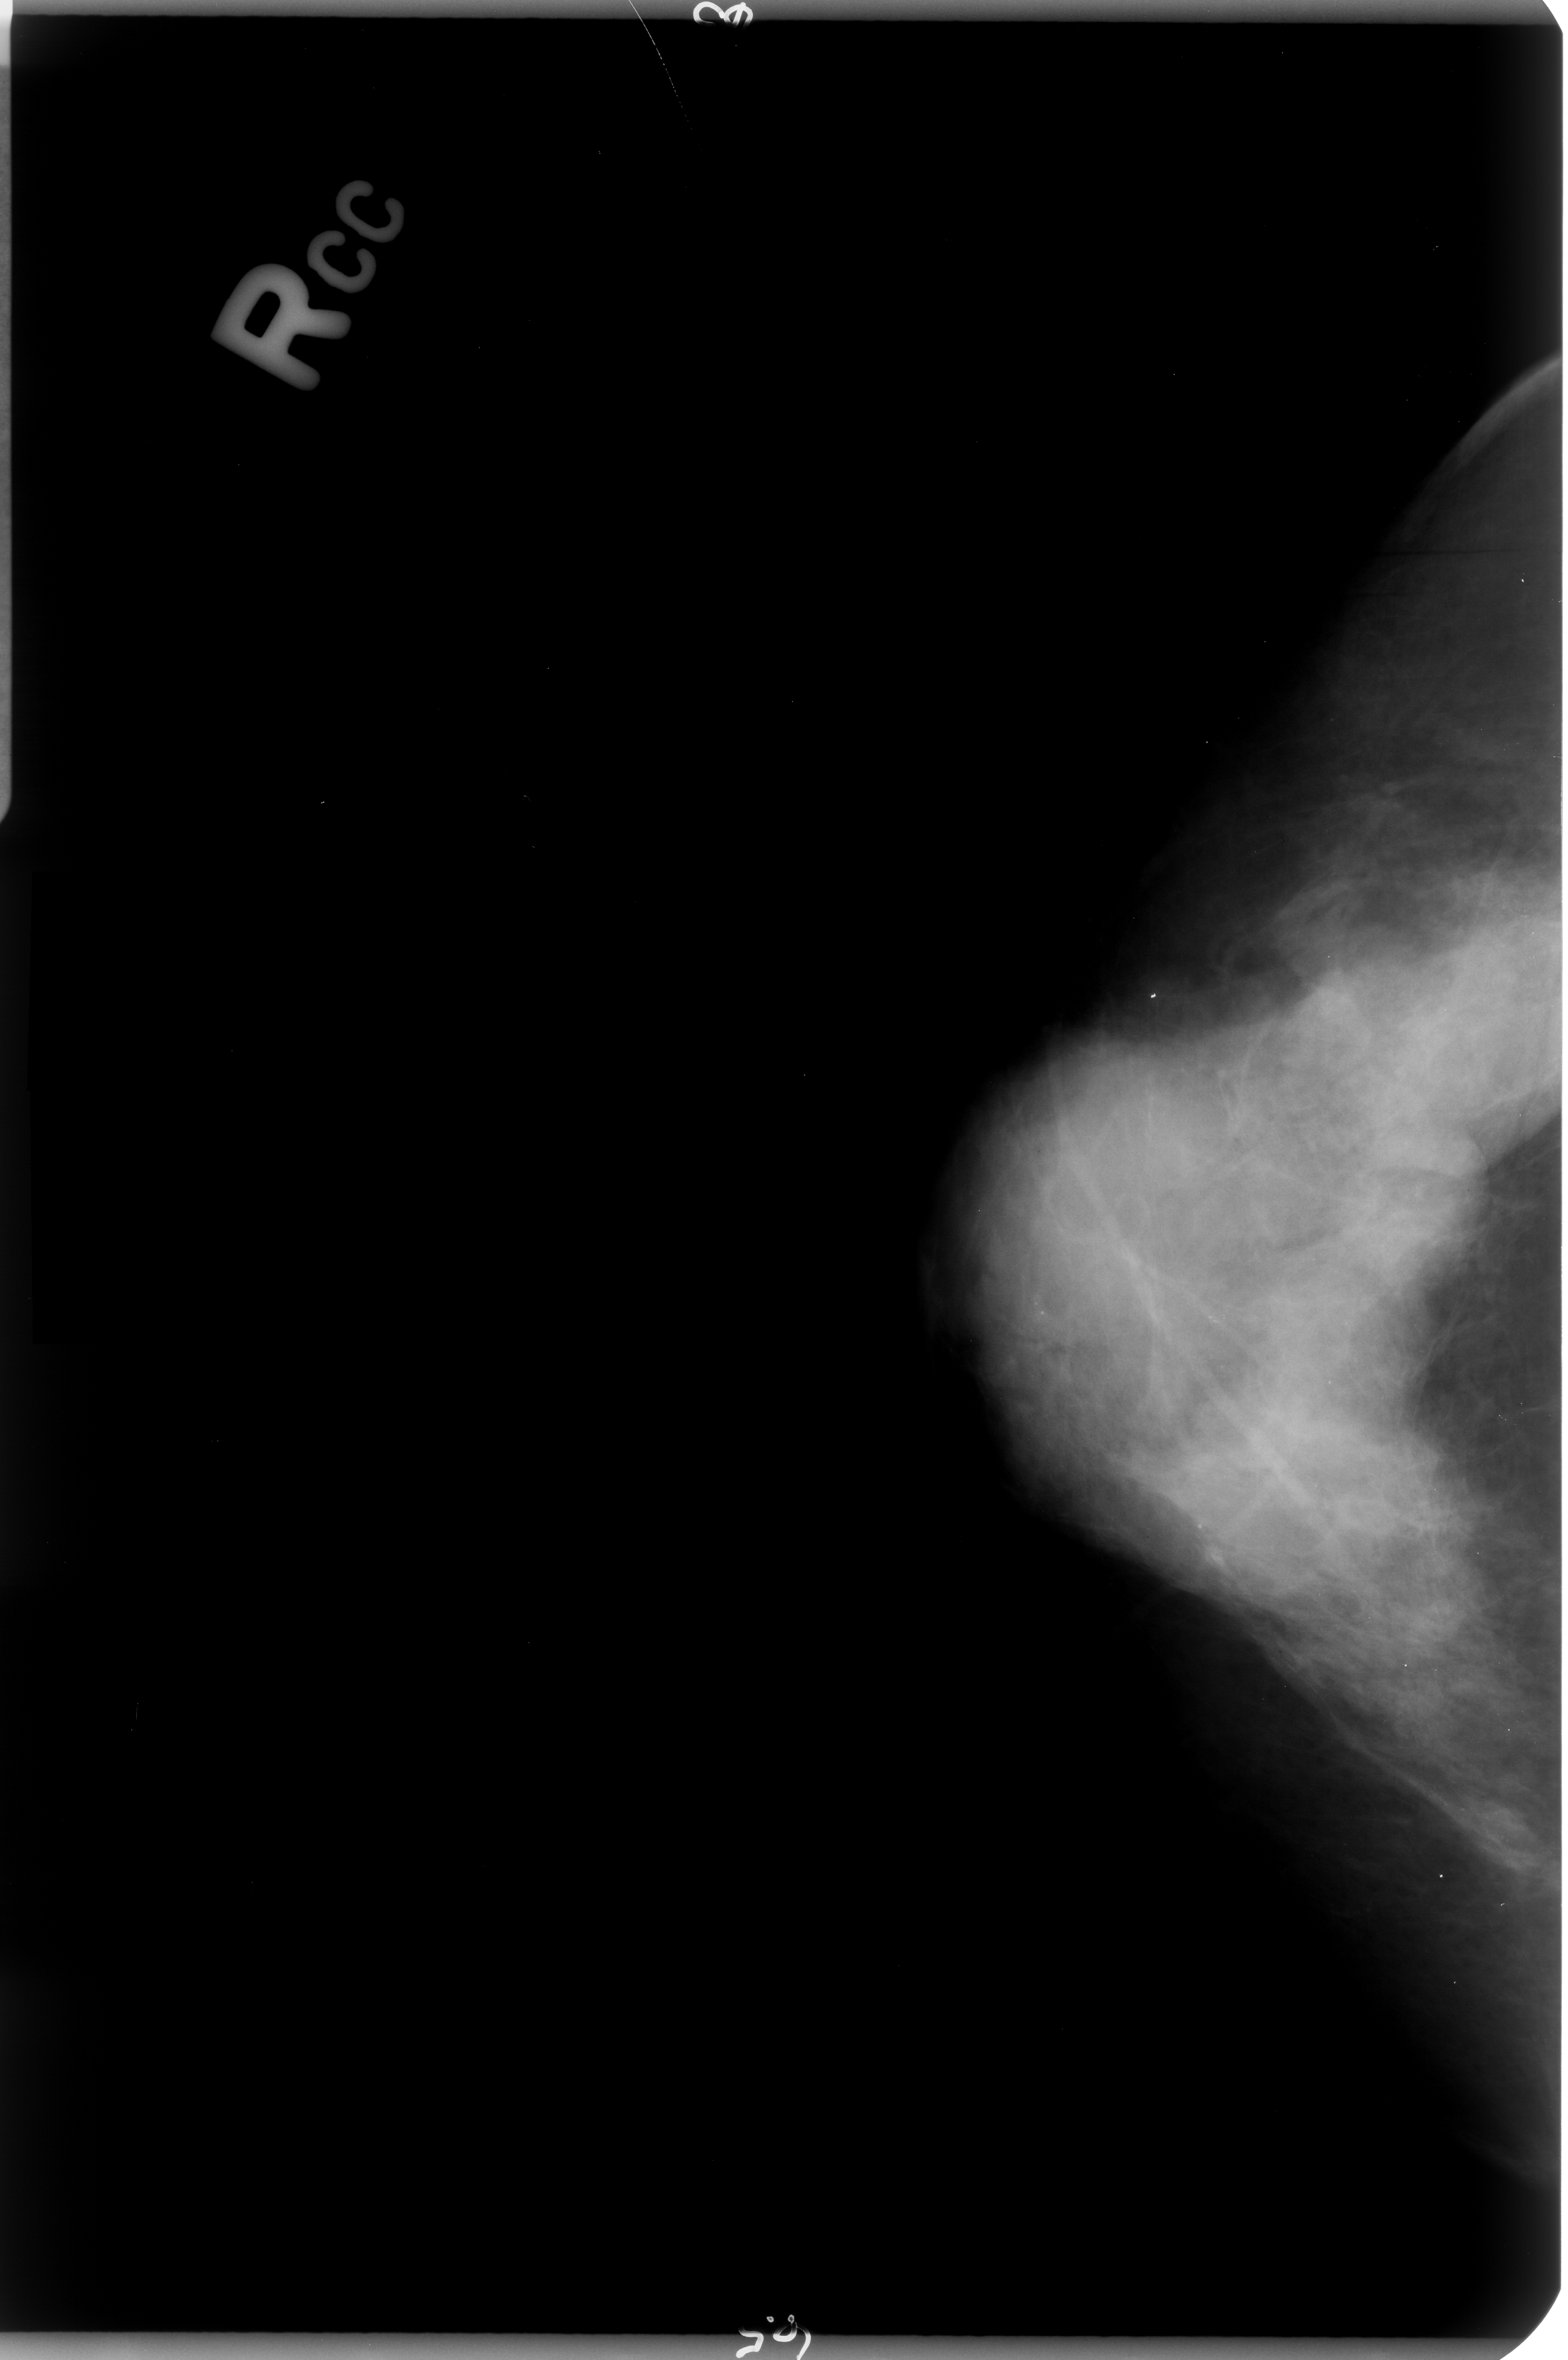
Mammogram (digitized film); right breast; CC view; breast composition: heterogeneously dense (BI-RADS density category 3 of 4).
- Abnormality record for this image: calcifications, morphology pleomorphic, distribution clustered; BI-RADS assessment category 4; pathology (as recorded): benign.